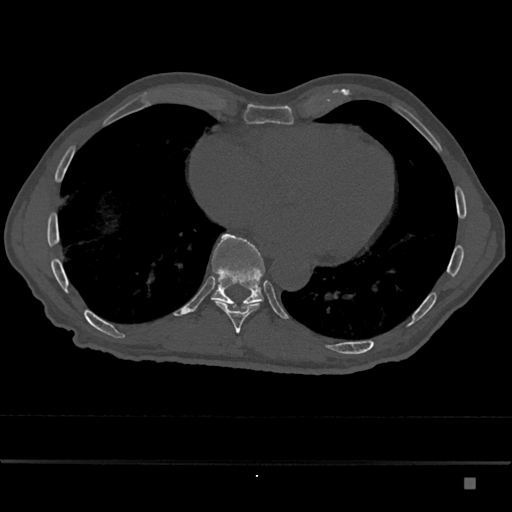
CT including the spine, one axial slice. Slice 778 of 797 in the series (ordered by position). Reconstruction kernel Br40s/3. 120 kVp. Bone window (W 1800 / L 400 HU). 0.5 mm slice thickness. 512 × 512 image matrix, field of view 390 × 390 mm. Patient: male, 72 years. From the clinical record (not read from this slice): primary cancer: prostate.
Outlined on this slice (semi-automatic segmentation, software-assisted and operator-edited):
- T10 vertebra: box from (x=211, y=234) to (x=265, y=309) px
- T9 vertebra: (x=215, y=302)–(x=260, y=334)